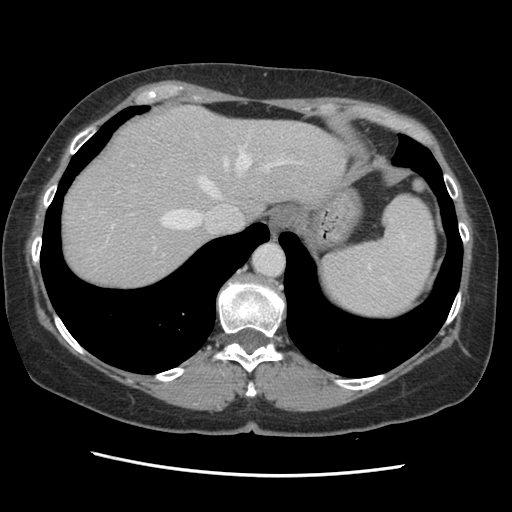
Contrast-enhanced abdominal CT, one axial slice. Soft-tissue window (W 400 / L 40 HU). 2.5 mm slice thickness. 512 × 512 image matrix, field of view 330 × 330 mm. Female patient, age 61 years. From the clinical record (not read from this slice): diagnosis: colorectal cancer liver metastases, imaged before liver resection; multiple liver metastases: no; largest metastasis: 2.4 cm.
Outlined on this slice (manually delineated by an expert):
- hepatic veins: bounding box <83,144,299,250> (left, top, right, bottom; pixels)
- liver: <61,105,346,291>
- planned liver remnant (the part of the liver to remain after resection): <61,105,346,291>
- portal vein (with intrahepatic branches): <112,223,164,255>